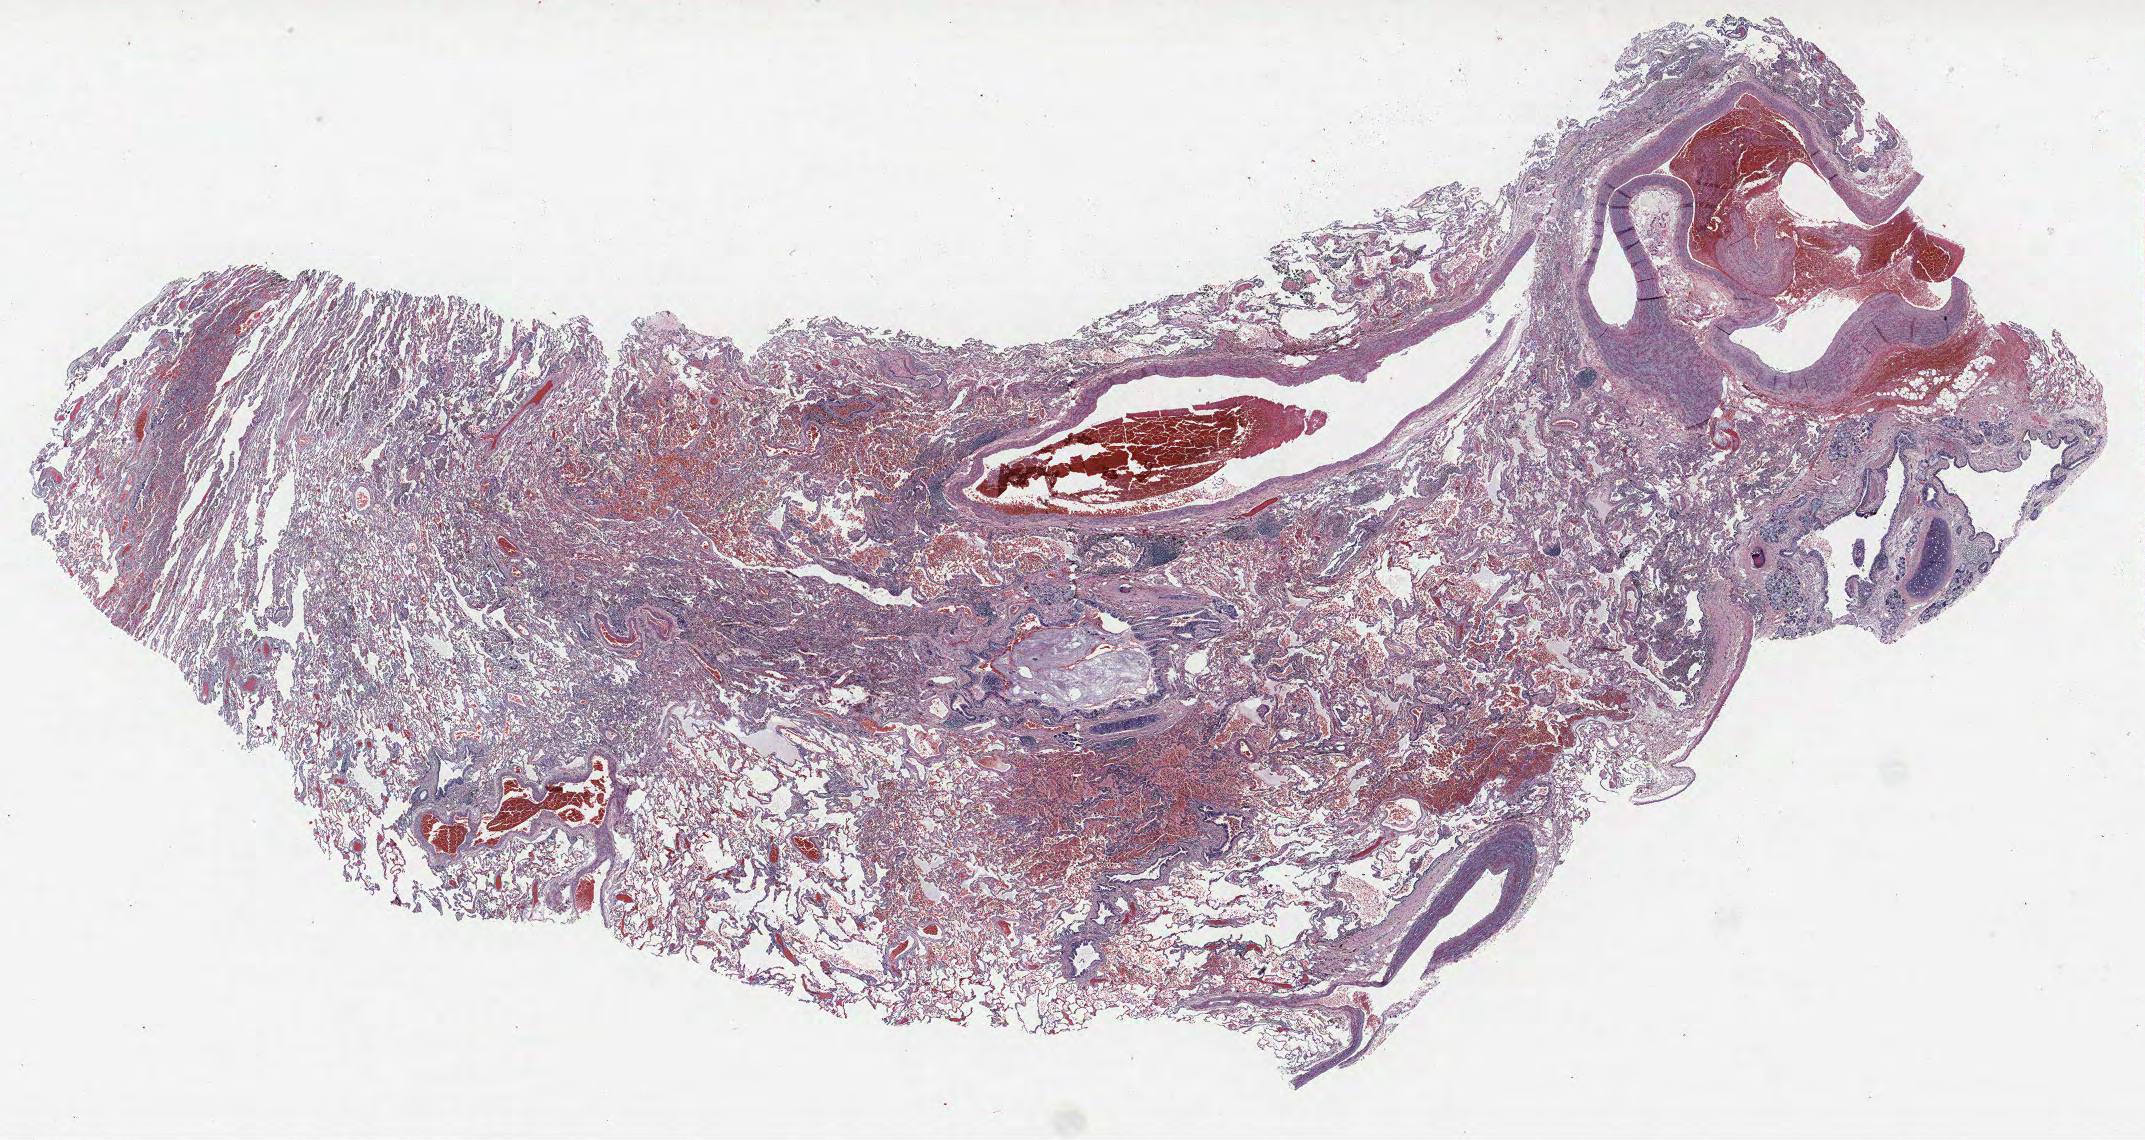
Hematoxylin and eosin (H&E) stained whole-slide image, shown as a low-resolution overview of the whole scanned area (about 34.3 x 18.2 mm). Formalin-fixed paraffin-embedded (FFPE) section. Lung tissue. Male, age 57 at enrolment. Current smoker at enrolment. Grade: moderately differentiated (G2).
Stage (AJCC 6th edition): IA. Participant's lung-cancer diagnosis: Adenocarcinoma, NOS. Tumour size (pathology): 11 mm. ICD-O-3 topography: lower lobe of lung (C34.3). Primary tumour location (clinical record): right lower lobe.